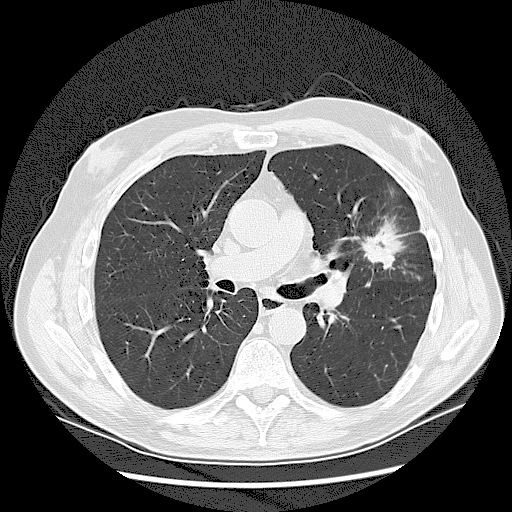
Chest CT (low-dose screening protocol), one axial image. First (baseline) screen. Lung window (W 1500 / L -600 HU). 2.5 mm slice thickness. Lung (sharp) reconstruction kernel (LUNG). 120 kVp. Slice 57 of 132 in the series. 512 × 512 image matrix. Male, age 65 years at enrolment.
• Lesion marked by an expert reader, bounding box (x1, y1, x2, y2) in pixels: (351, 226, 398, 270).
• Screening reader's record for this exam (one nodule recorded; not confirmed to be the boxed lesion): non-calcified nodule or mass ≥4 mm, left upper lobe, 37 × 27 mm, spiculated (stellate) margins, soft tissue attenuation.
• Lung cancer was diagnosed 56 days after this screen: non-small cell carcinoma, poorly differentiated (G3), stage IA (AJCC 6th edition).